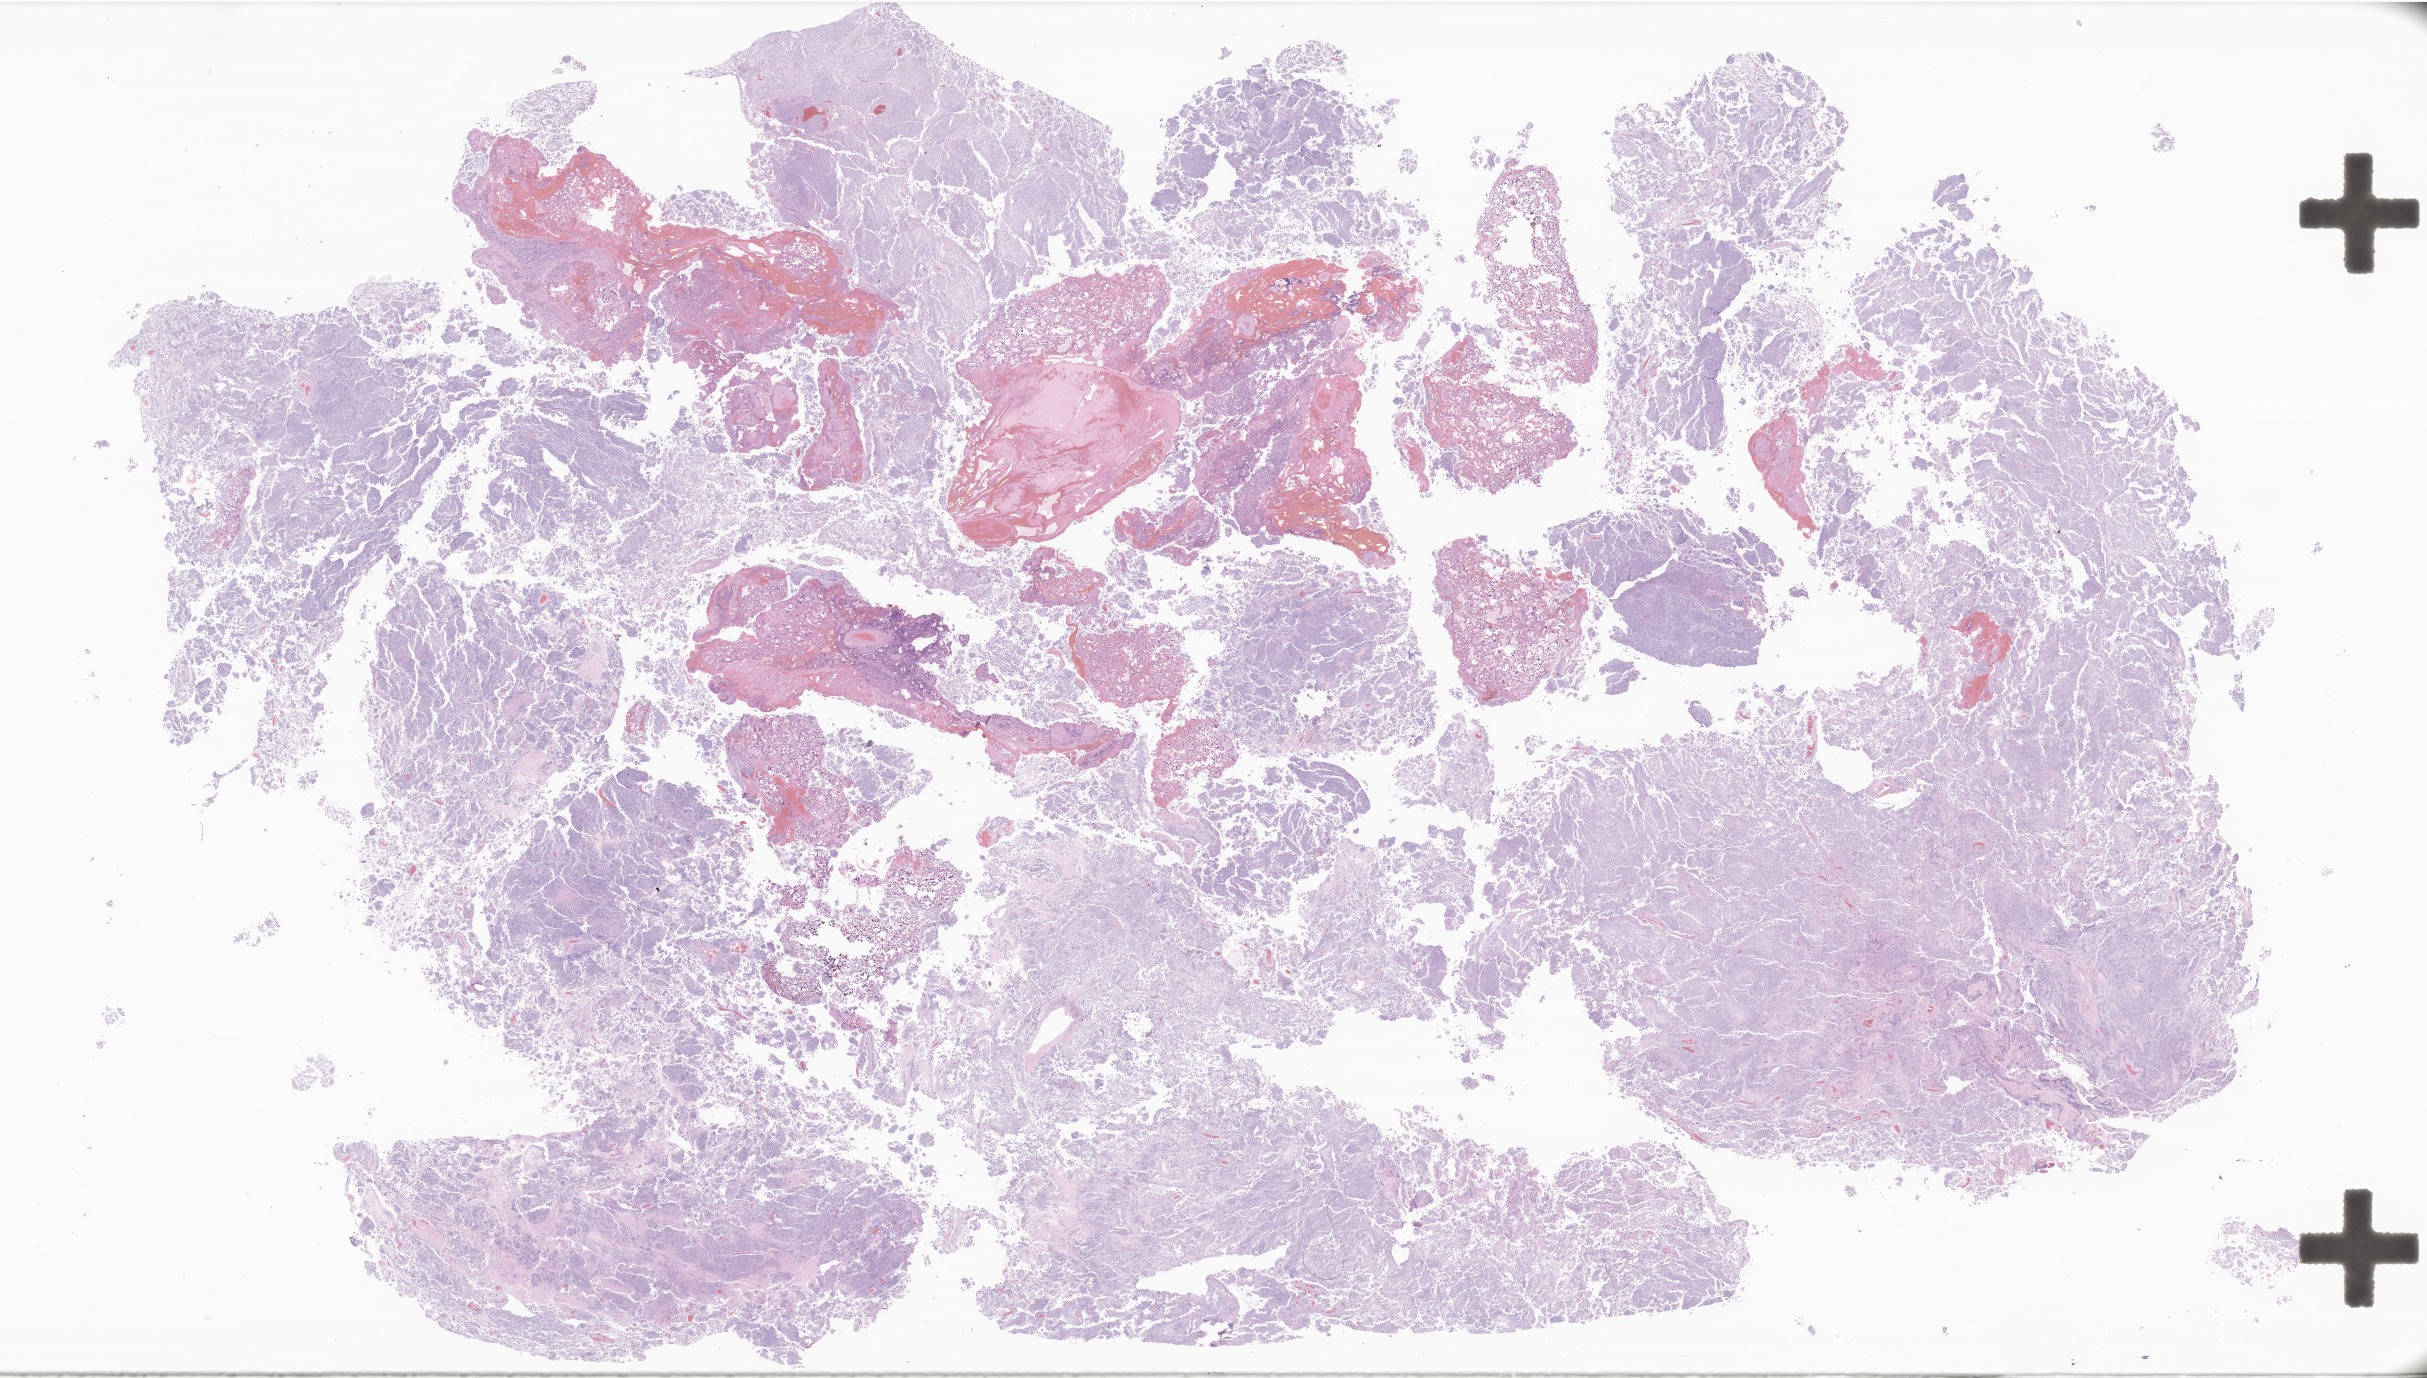
Haematoxylin and eosin whole-slide image of tumor tissue from the brain, low-resolution overview of the scanned area, about 40.9 x 23.2 mm; FFPE section. Patient: female, age 152 months (12 years 8 months).
Diagnosis (ICD-O-3 morphology term): Medulloblastoma, NOS.